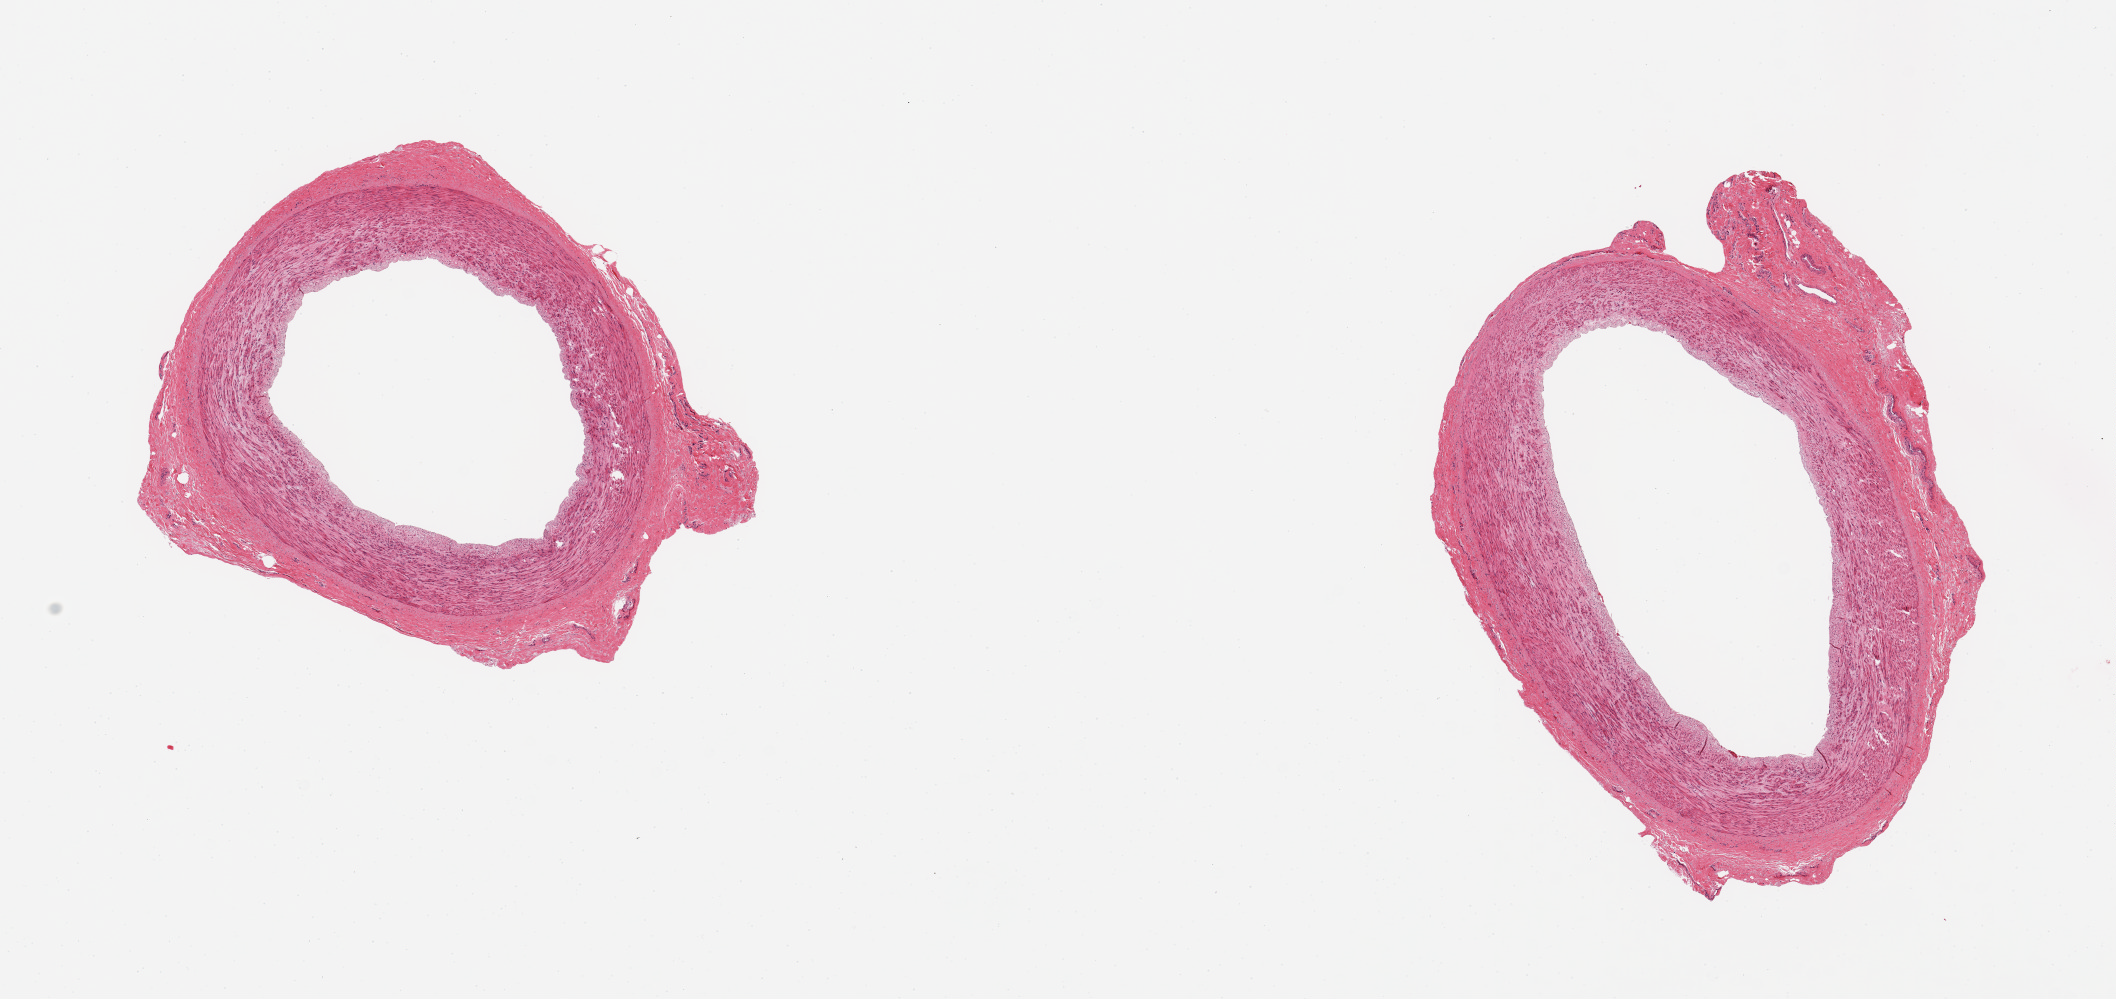
Whole-slide image, haematoxylin and eosin stain, brightfield, shown as a low-resolution overview of the whole scanned area (about 16.7 x 7.9 mm, slide scanned at 20x); PAXgene-fixed paraffin-embedded (PFPE) section; target tissue: tibial artery; tissue donor sample.
• pathologist's review note for this sample: 2 pieces; eccentric plaque; 30% external fat